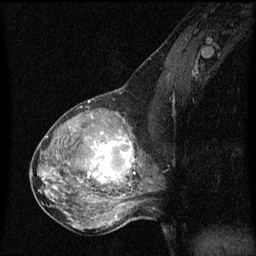
Breast MRI (dynamic contrast-enhanced), one sagittal slice. Slice 32 of 60 in the series (ordered by position). Dynamic contrast-enhanced series, image 2 of 3 at this slice position (ordered by acquisition). 1.5 T. TE 4.2 ms, TR 8 ms. 2 mm slice thickness. 256 × 256 image matrix, field of view 200 × 200 mm. Patient: female, 50 years.
Annotated regions visible in this slice (semi-automatically segmented with operator editing):
- analysis volume of interest (the breast-tissue region the enhancement analysis was run in; not a lesion): bounding box (x1, y1, x2, y2) in pixels: (91, 126, 141, 189)
- tumour enhancement mask (voxels above the 70 % enhancement threshold inside the analysis volume of interest): (93, 138, 134, 183)